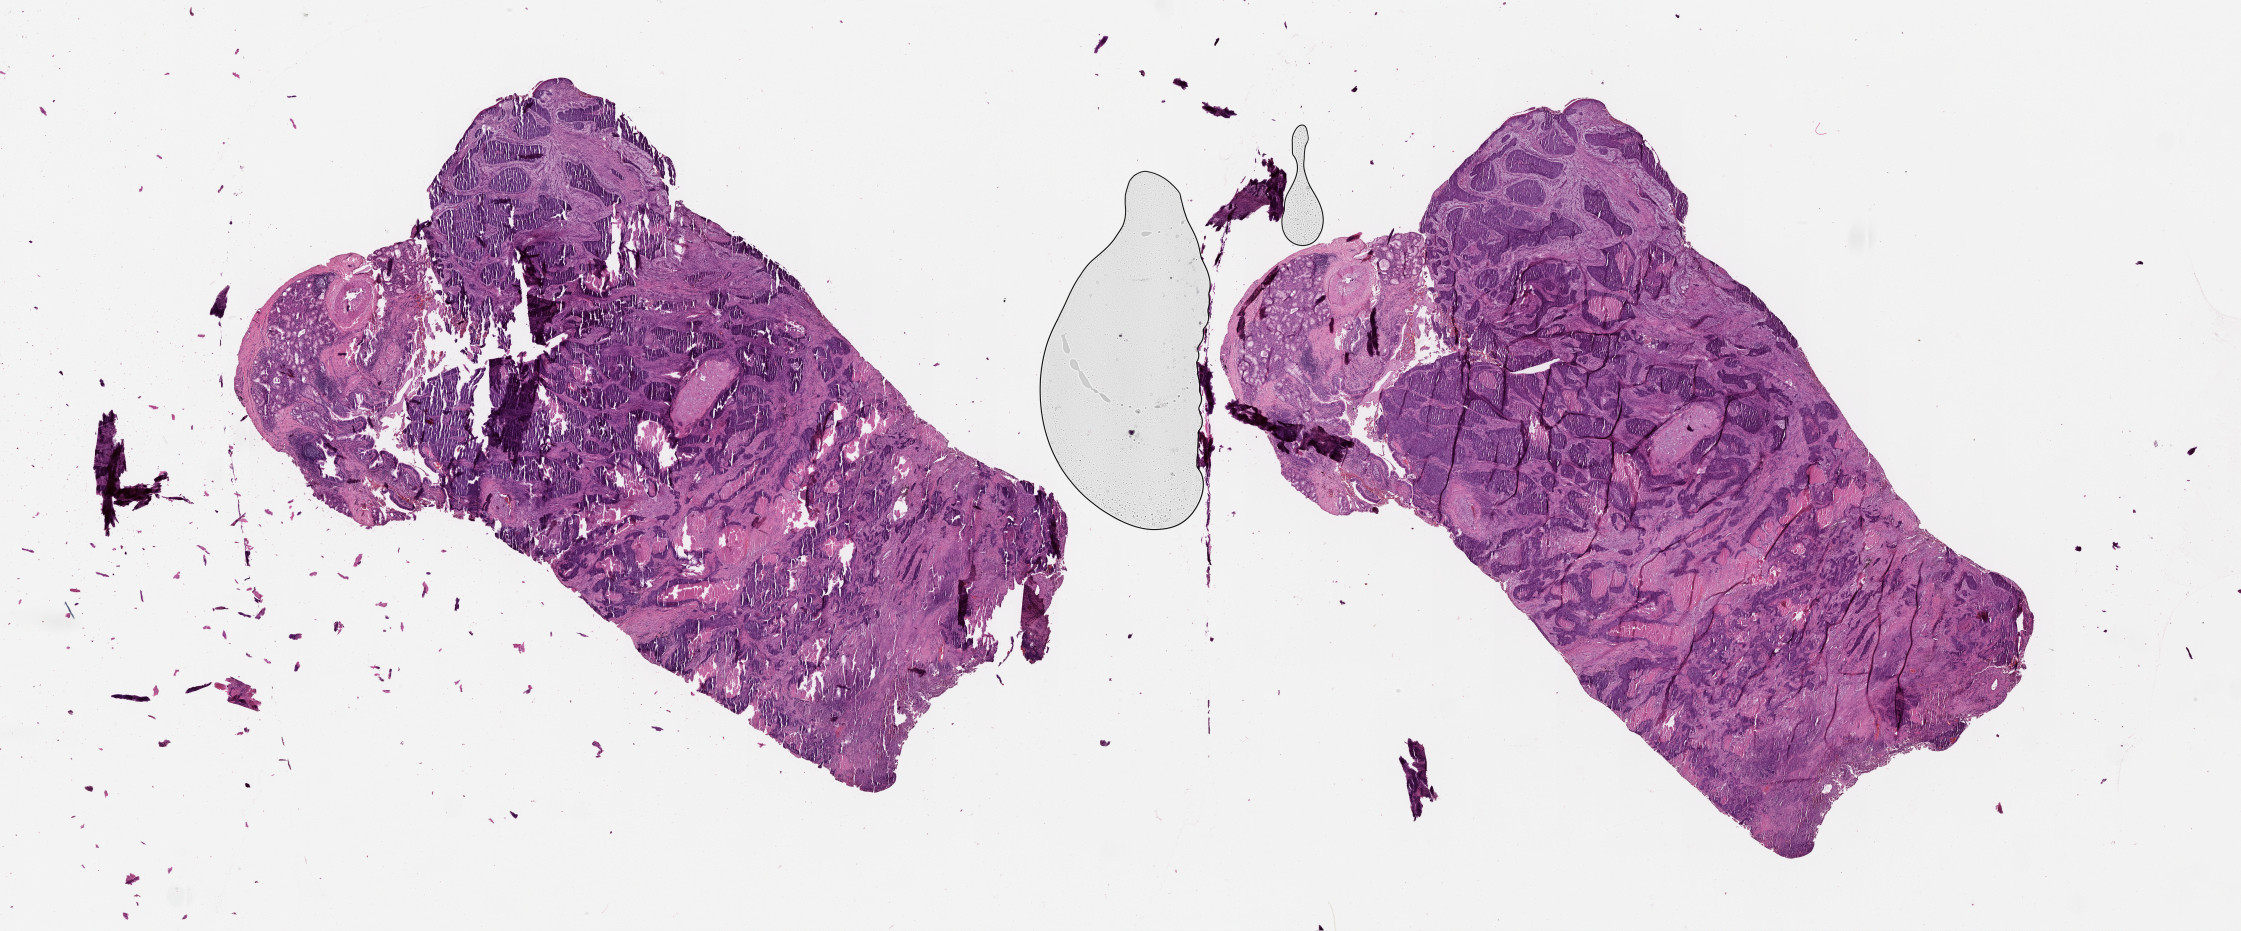
Digitized H&E tissue section (whole slide) — shown as a low-resolution overview of the whole scanned area (about 36.1 x 15.0 mm, acquisition: 20x scan). Tumour tissue sample, lung. 59-year-old male patient.
Patient diagnosis (cohort enrolment): squamous cell carcinoma (lung).